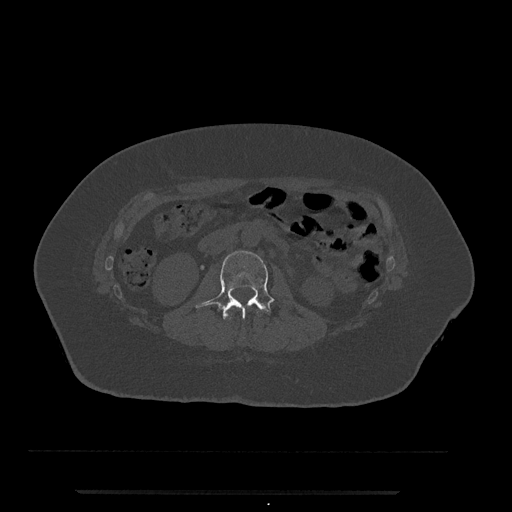
CT including the spine, one axial slice; slice 40 of 797 in the series (ordered by position); reconstruction kernel Br40s/3; 120 kVp; bone window (W 1800 / L 400 HU); 512 × 512 image matrix. Female patient, age 51 years. Case-level facts recorded for this patient, not image findings: primary cancer: neuro.
Outlined on this slice (semi-automatic segmentation, software-assisted and operator-edited):
- L1 vertebra: bounding box [x1, y1, x2, y2] px = [227, 309, 259, 320]
- L2 vertebra: [195, 250, 275, 321]